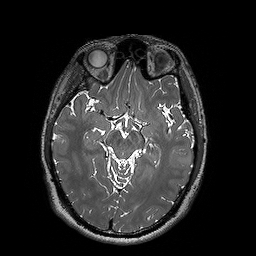
Brain MRI from a brain-tumour surgery series, one axial slice. Position 100 of 192 along the scan axis. 1 mm slice thickness. 256 × 256 image matrix. From the clinical record (not read from this slice): histopathology: Oligodendroglioma; WHO grade: 2.
Outlined on this slice (outlined manually by an expert reader):
- tumour: bounding box [x1, y1, x2, y2] px = [181, 156, 193, 164]